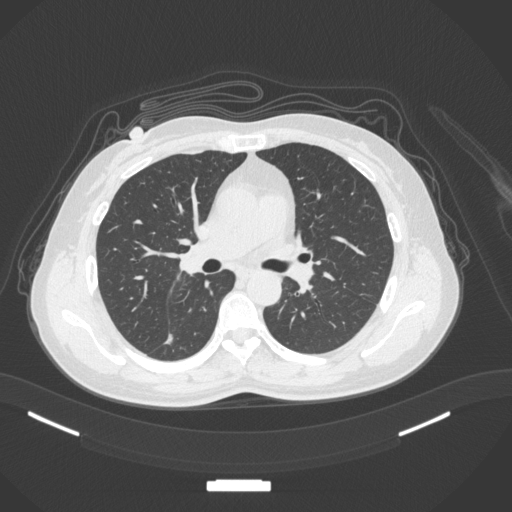
Chest CT, one axial slice; slice 180 of 352 in the series (ordered by position); lung window (W 1500 / L -600 HU); 1 mm slice thickness; 512 × 512 image matrix, field of view 400 × 400 mm. Female patient, age 55 years. Case-level facts recorded for this patient, not image findings: clinical TNM (as recorded): T1c N1 M0.
Outlined on this slice (bounding box drawn by a radiologist):
- lung tumour (recorded histology: adenocarcinoma): bounding box [x1, y1, x2, y2] px = [159, 331, 184, 355]